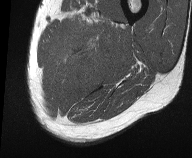
MRI of an extremity soft-tissue mass, one axial slice; slice 12 of 61 in the series (ordered by position); MR volume resampled by the dataset authors to the PET/CT grid (not the native acquisition matrix); 192 × 158 image matrix, field of view 187 × 154 mm. Male patient. From the clinical record (not read from this slice): histological type: pleiomorphic liposarcoma; grade: high; site of the primary tumour: left thigh.
Annotated regions visible in this slice (expert contour drawn on MRI and transferred to this co-registered scan by the dataset authors):
- gross tumour volume including surrounding oedema: box from (x=64, y=16) to (x=117, y=83) px